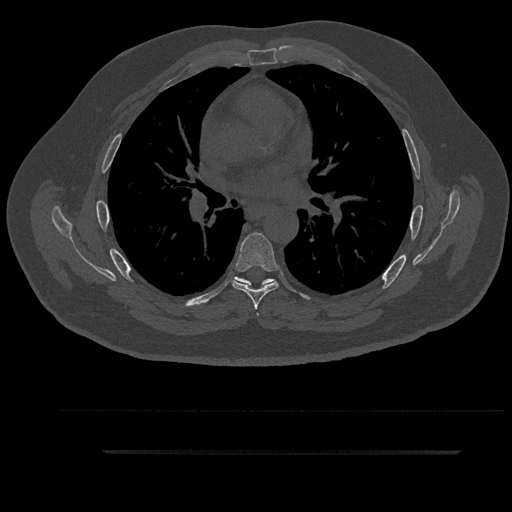
CT including the spine, one axial slice; 120 kVp; bone window (W 1800 / L 400 HU); 512 × 512 image matrix, field of view 432 × 432 mm. Patient: male, 63 years. From the clinical record (not read from this slice): primary cancer: renal.
Annotated regions visible in this slice (semi-automatically segmented with operator editing):
- T5 vertebra: bounding box <235,277,266,316> (left, top, right, bottom; pixels)
- T6 vertebra: <232,232,279,310>
- T7 vertebra: <240,278,276,286>